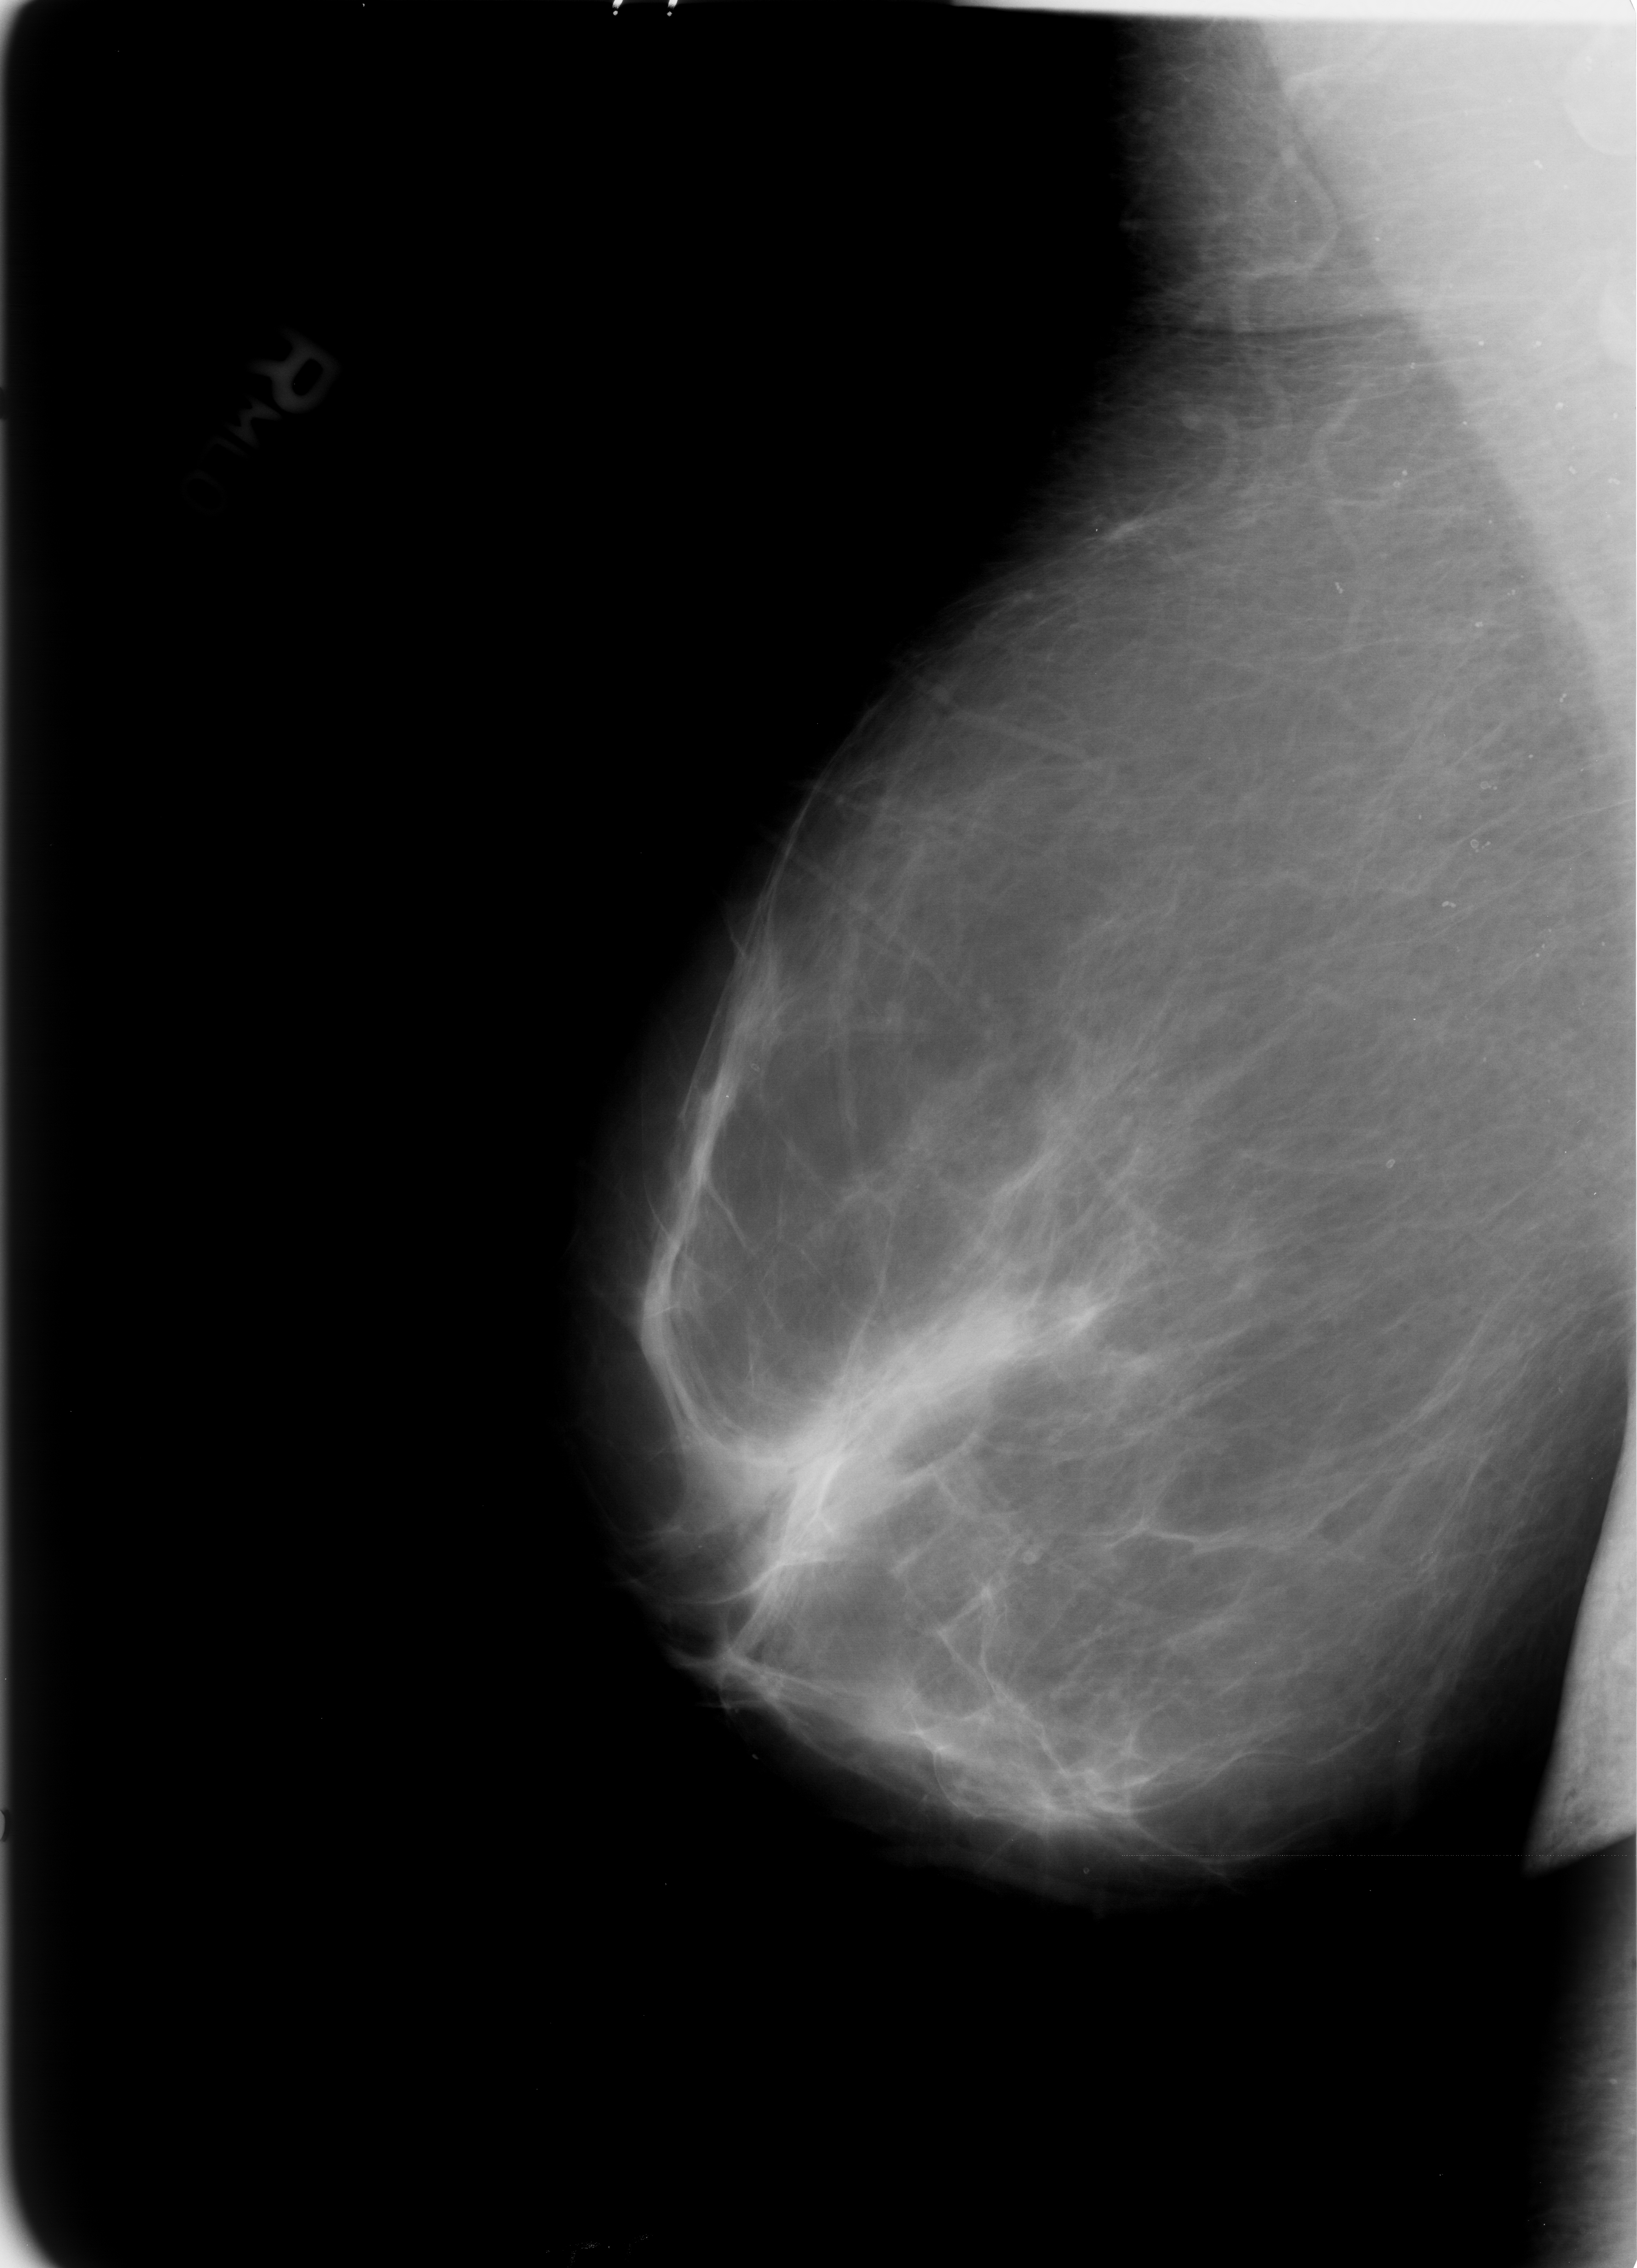
Digitized screen-film mammogram, right breast, MLO view, BI-RADS breast density category 2 (scale 1–4).
- Marked abnormality: calcifications, morphology skin, distribution regional; BI-RADS assessment category 2; benign without callback (not worked up further).